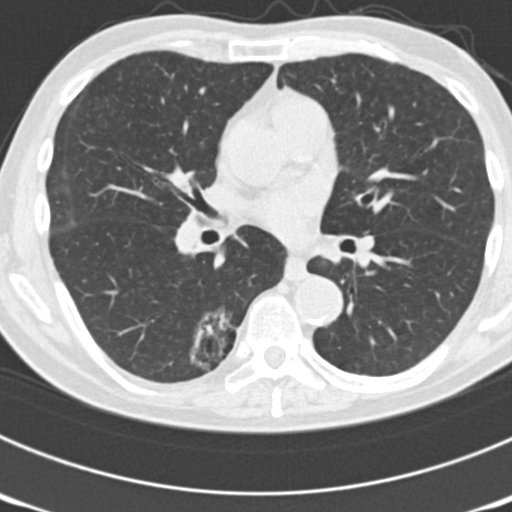
Axial slice from a low-dose chest CT screening exam, third annual screen, lung window (W 1500 / L -600 HU), 2 mm slice thickness, standard (soft-tissue) reconstruction kernel (B30f), 120 kVp, slice 80 of 177 in the series. Male, age 70 years at enrolment. Current smoker at enrolment.
• Lesion marked by an expert reader, bounding box (x1, y1, x2, y2) in pixels: (147, 303, 238, 384).
• The screening reader recorded 3 non-calcified nodules or masses ≥4 mm on this exam (right upper lobe, left upper lobe, right lower lobe); which of them this box marks is not recorded.
• Official screen result: positive, other.
• Lung cancer was diagnosed 14 days after this screen: bronchiolo-alveolar adenocarcinoma, NOS, right lower lobe, poorly differentiated (G3), stage IB (AJCC 6th edition), 30 mm at pathology.